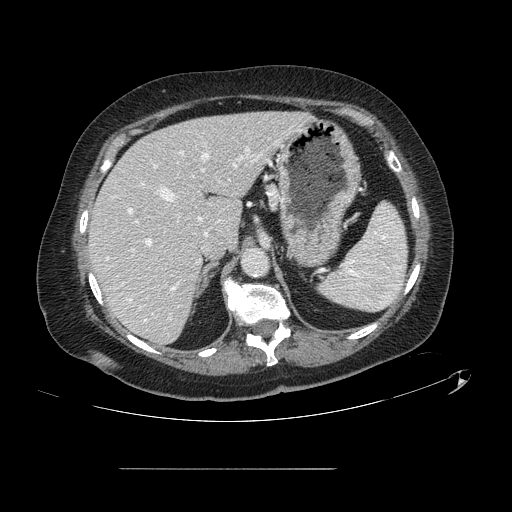
Contrast-enhanced abdominal CT, one axial slice; position 89 of 148 along the scan axis; 120 kVp; intravenous contrast given; soft-tissue window (W 400 / L 40 HU); 2.5 mm slice thickness; 512 × 512 image matrix, field of view 439 × 439 mm. Female patient, age 75 years. From the clinical record (not read from this slice): diagnosis: colorectal cancer liver metastases, imaged before liver resection.
Structures marked on this image (outlined manually by an expert reader):
- hepatic veins: box from (x=129, y=152) to (x=208, y=321) px
- liver: (x=90, y=113)–(x=308, y=343)
- planned liver remnant (the part of the liver to remain after resection): (x=90, y=112)–(x=308, y=343)
- portal vein (with intrahepatic branches): (x=128, y=146)–(x=263, y=290)